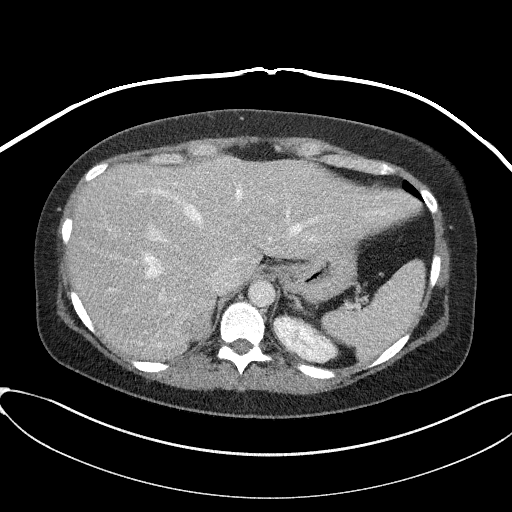
Contrast-enhanced abdominal CT, one axial slice. Position 66 of 95 along the scan axis. Intravenous contrast given. Soft-tissue window (W 400 / L 40 HU). 3 mm slice thickness. 512 × 512 image matrix, field of view 410 × 410 mm. Patient: female, 46 years. From the clinical record (not read from this slice): diagnosis: adrenocortical carcinoma; tumour side: right adrenal; tumour size at pathology: 7.2 cm; Ki-67 index: 50 %; stage (as recorded): 4.
Annotated regions visible in this slice (semi-automatically segmented with operator editing):
- mass: bounding box [x1, y1, x2, y2] px = [183, 311, 210, 338]